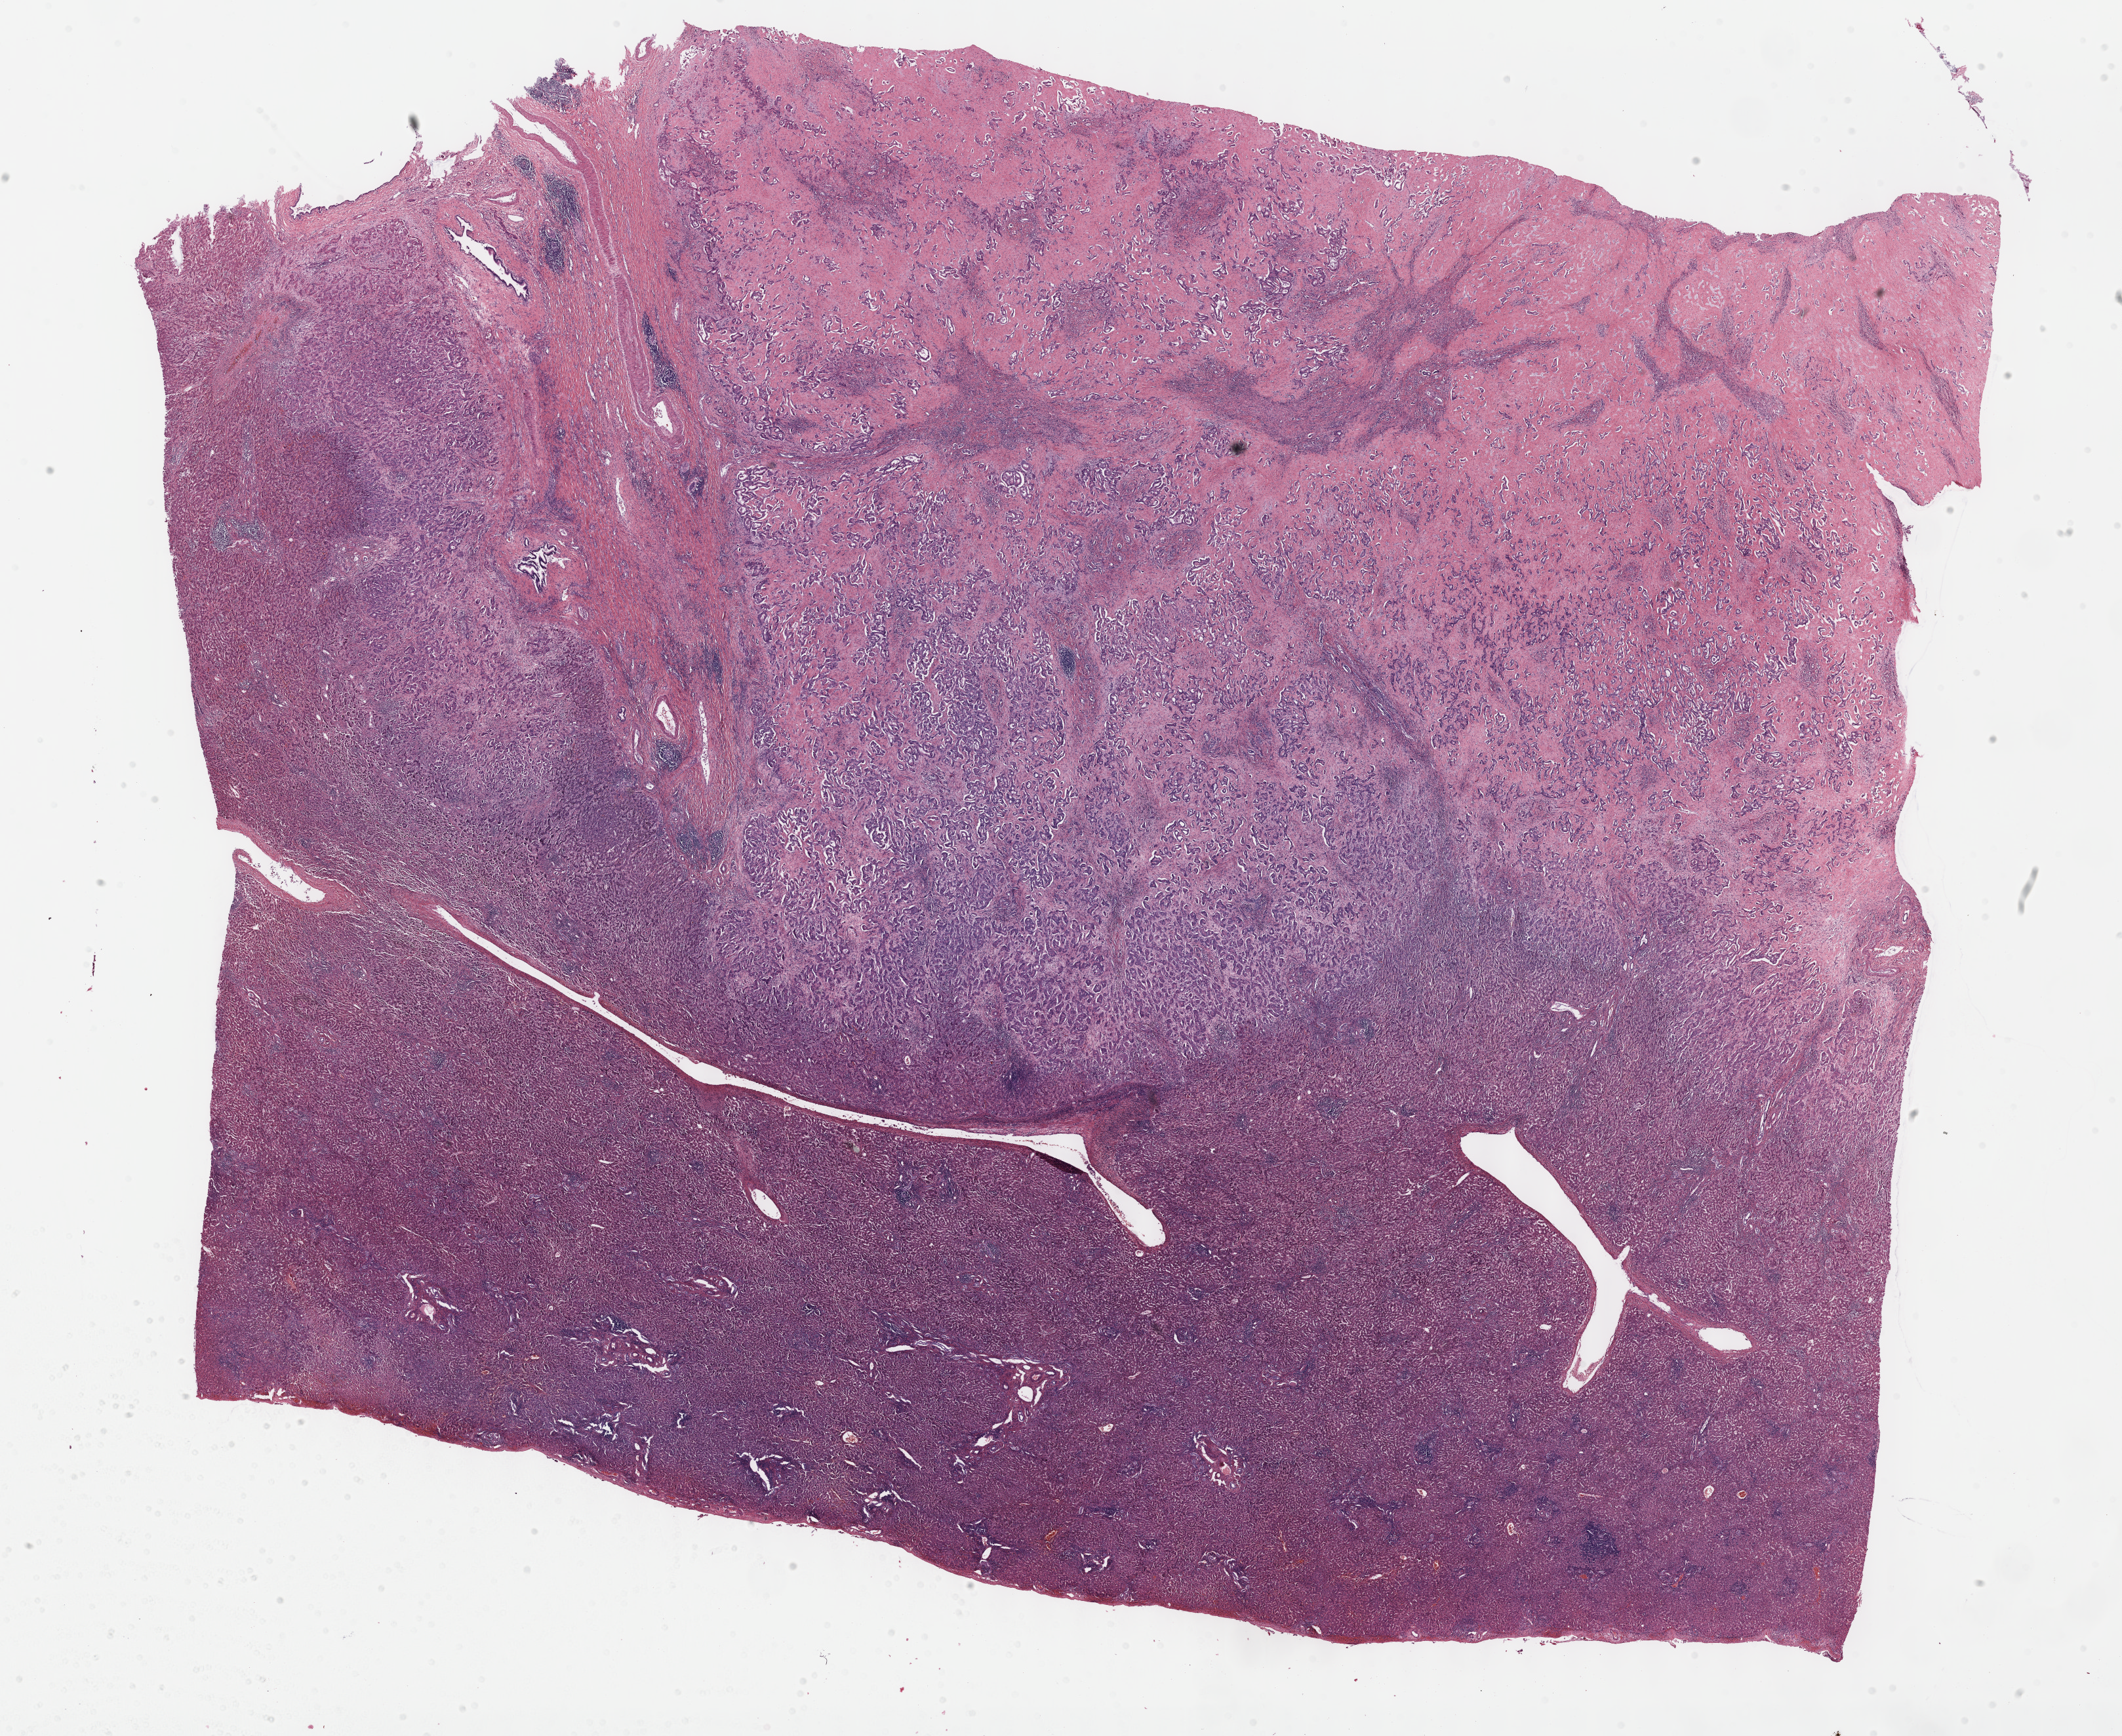
Whole-slide histology image, H&E, whole scanned area (about 26.2 x 21.4 mm) shown as a low-resolution overview, formalin-fixed paraffin-embedded (FFPE) diagnostic section, sample: primary tumour, bile duct. Patient: male, age at initial diagnosis 52 years. Histologic grade: G2 (moderately differentiated).
AJCC pathologic stage: IV (6th edition). Histologic diagnosis: Cholangiocarcinoma (extrahepatic bile duct).